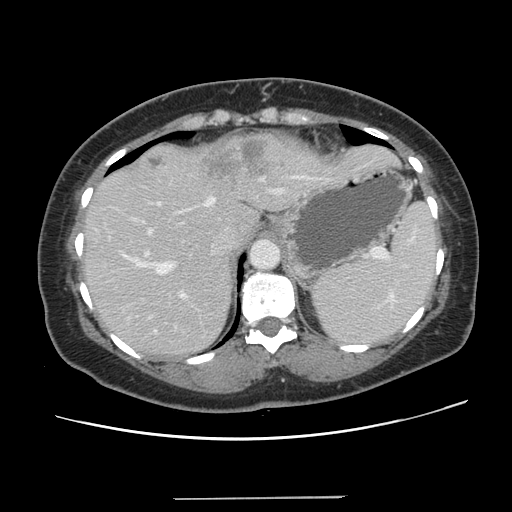
Contrast-enhanced abdominal CT, one axial slice; slice 99 of 141 in the series (ordered by position); 120 kVp; intravenous contrast given; soft-tissue window (W 400 / L 40 HU); 2.5 mm slice thickness; 512 × 512 image matrix. Female patient, age 53 years. From the clinical record (not read from this slice): diagnosis: colorectal cancer liver metastases, imaged before liver resection; multiple liver metastases: no; largest metastasis: 14.5 cm; disease in both lobes: yes.
Annotated regions visible in this slice (manually delineated by an expert):
- hepatic veins: bounding box <125,175,328,273> (left, top, right, bottom; pixels)
- liver: <84,133,398,356>
- planned liver remnant (the part of the liver to remain after resection): <84,209,260,356>
- portal vein (with intrahepatic branches): <130,189,281,319>
- liver metastasis: <151,157,164,168>
- liver metastasis: <203,137,269,182>